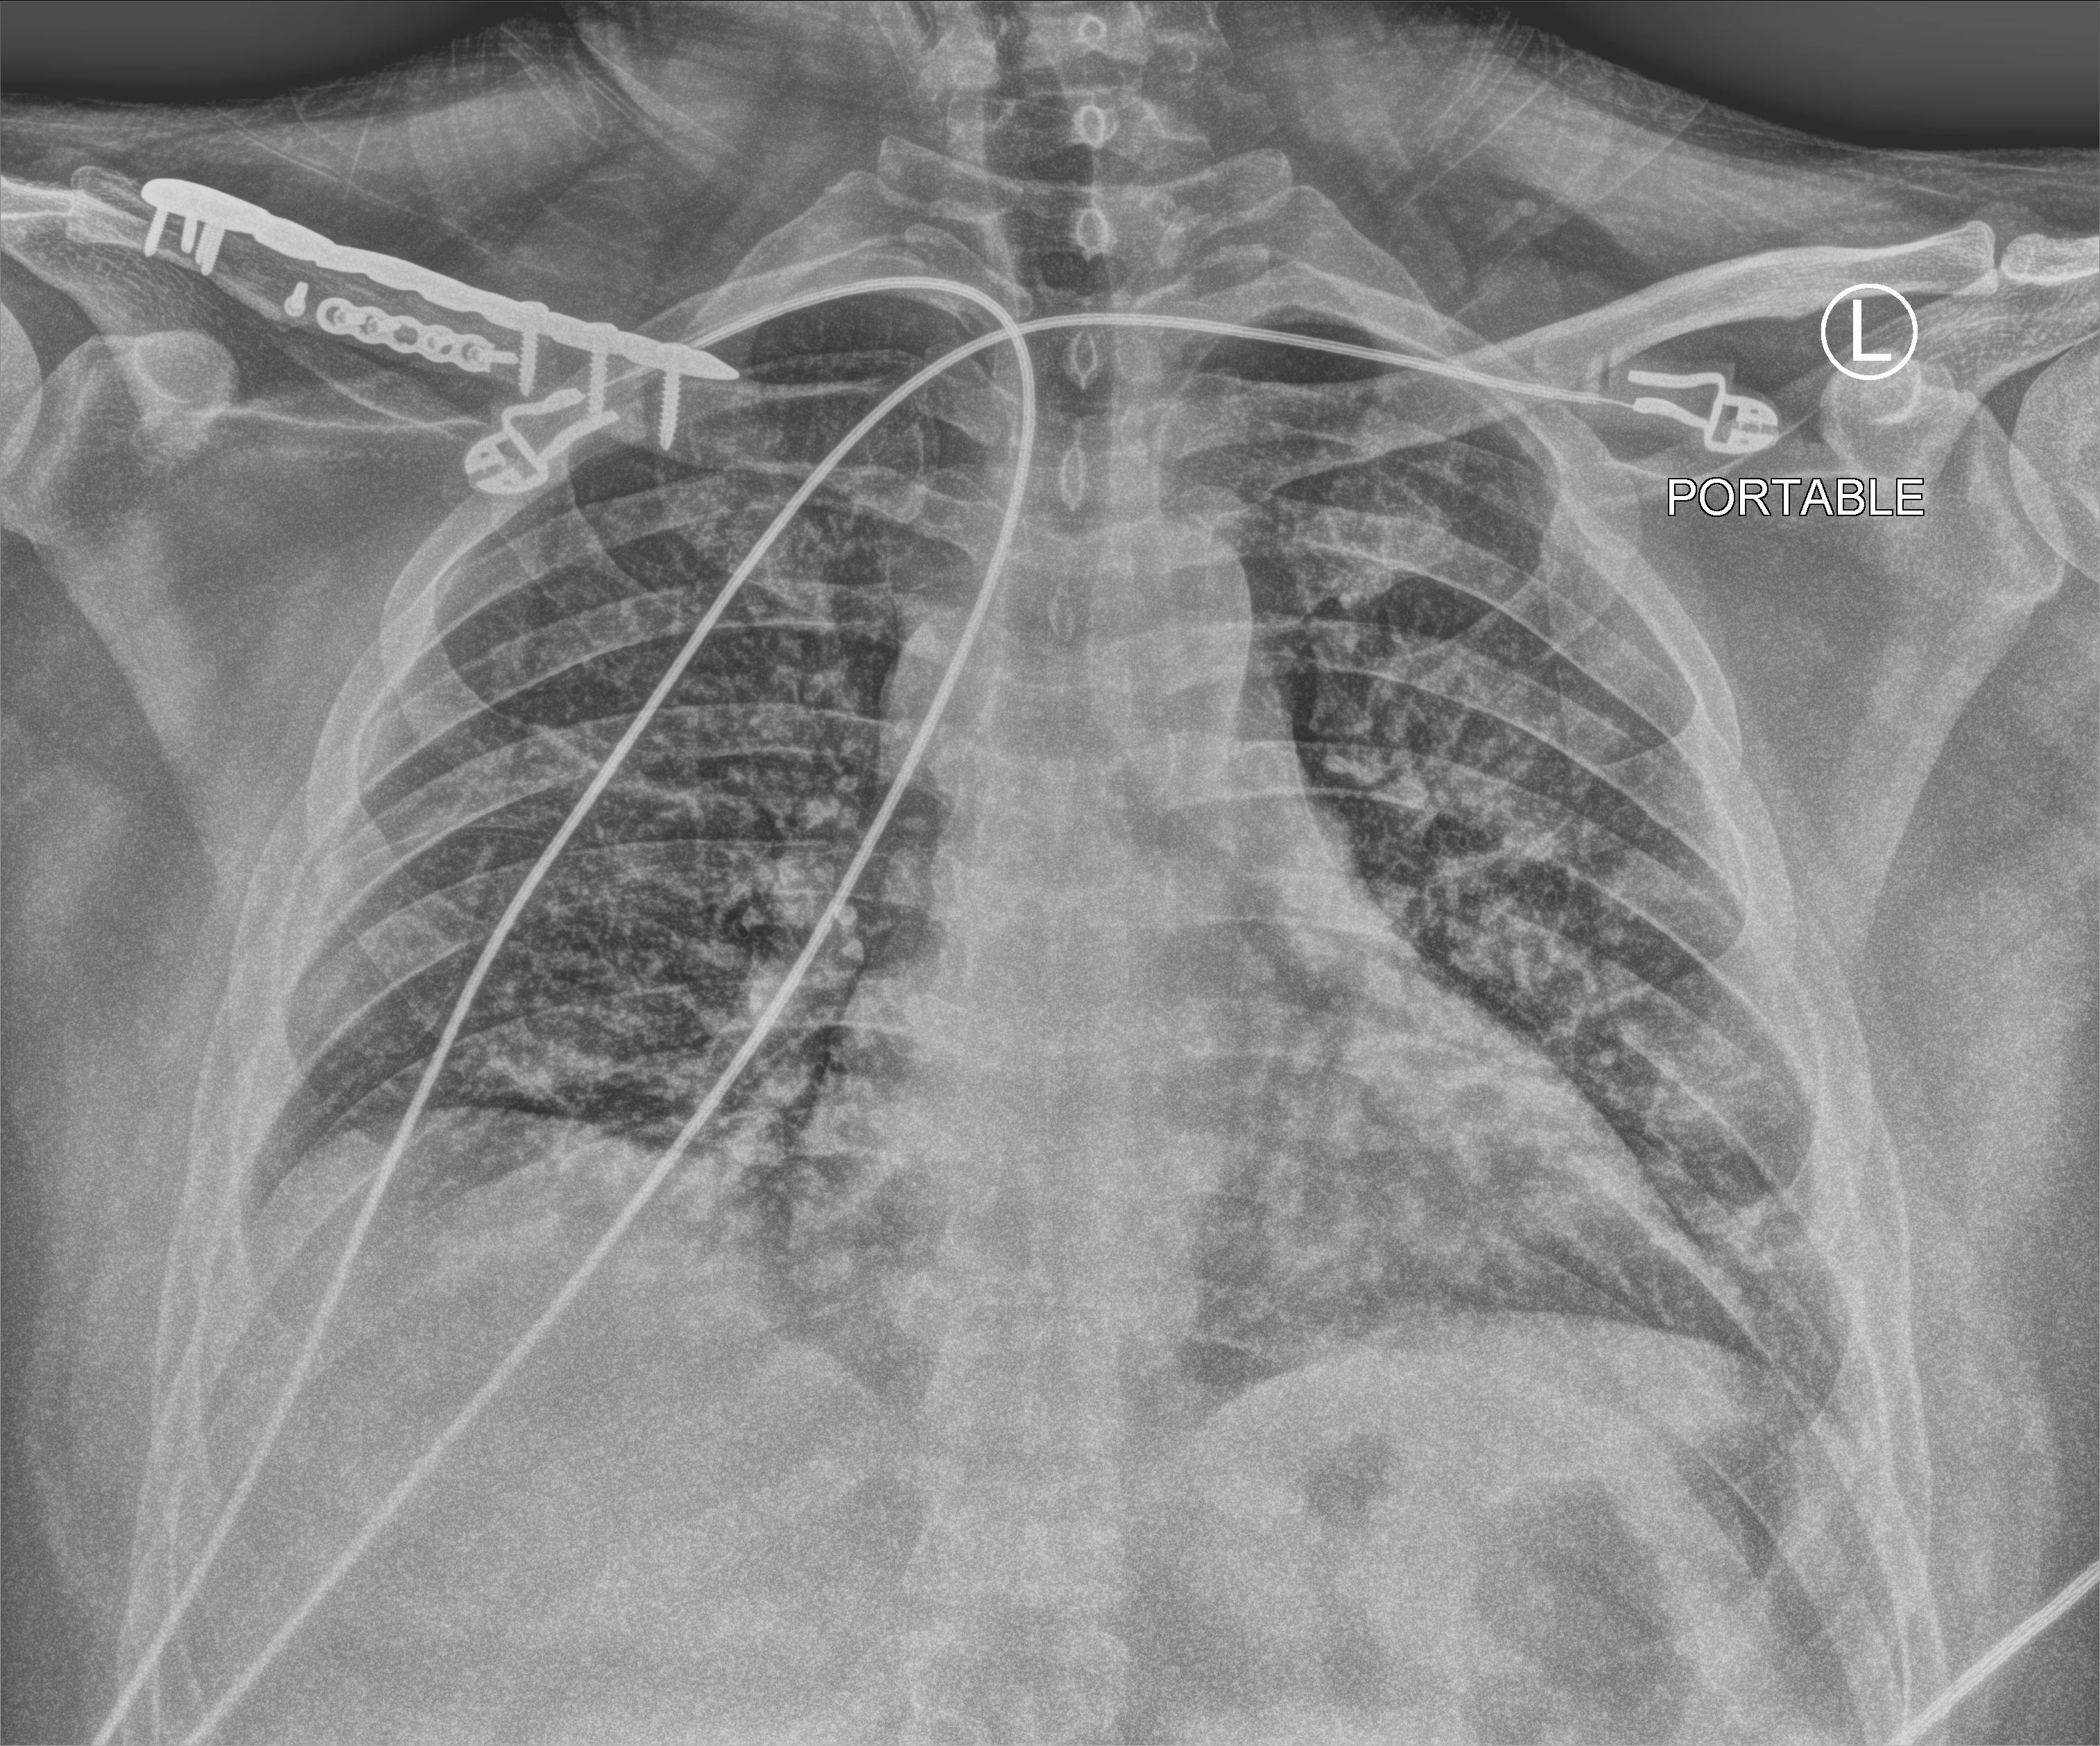
Portable chest radiograph; anteroposterior (AP) projection. Male patient hospitalised with COVID-19, age 18–59 years.
Admission-level facts for this patient (not findings on this image; timing relative to this image not recorded): admitted to intensive care during this hospital stay: no.